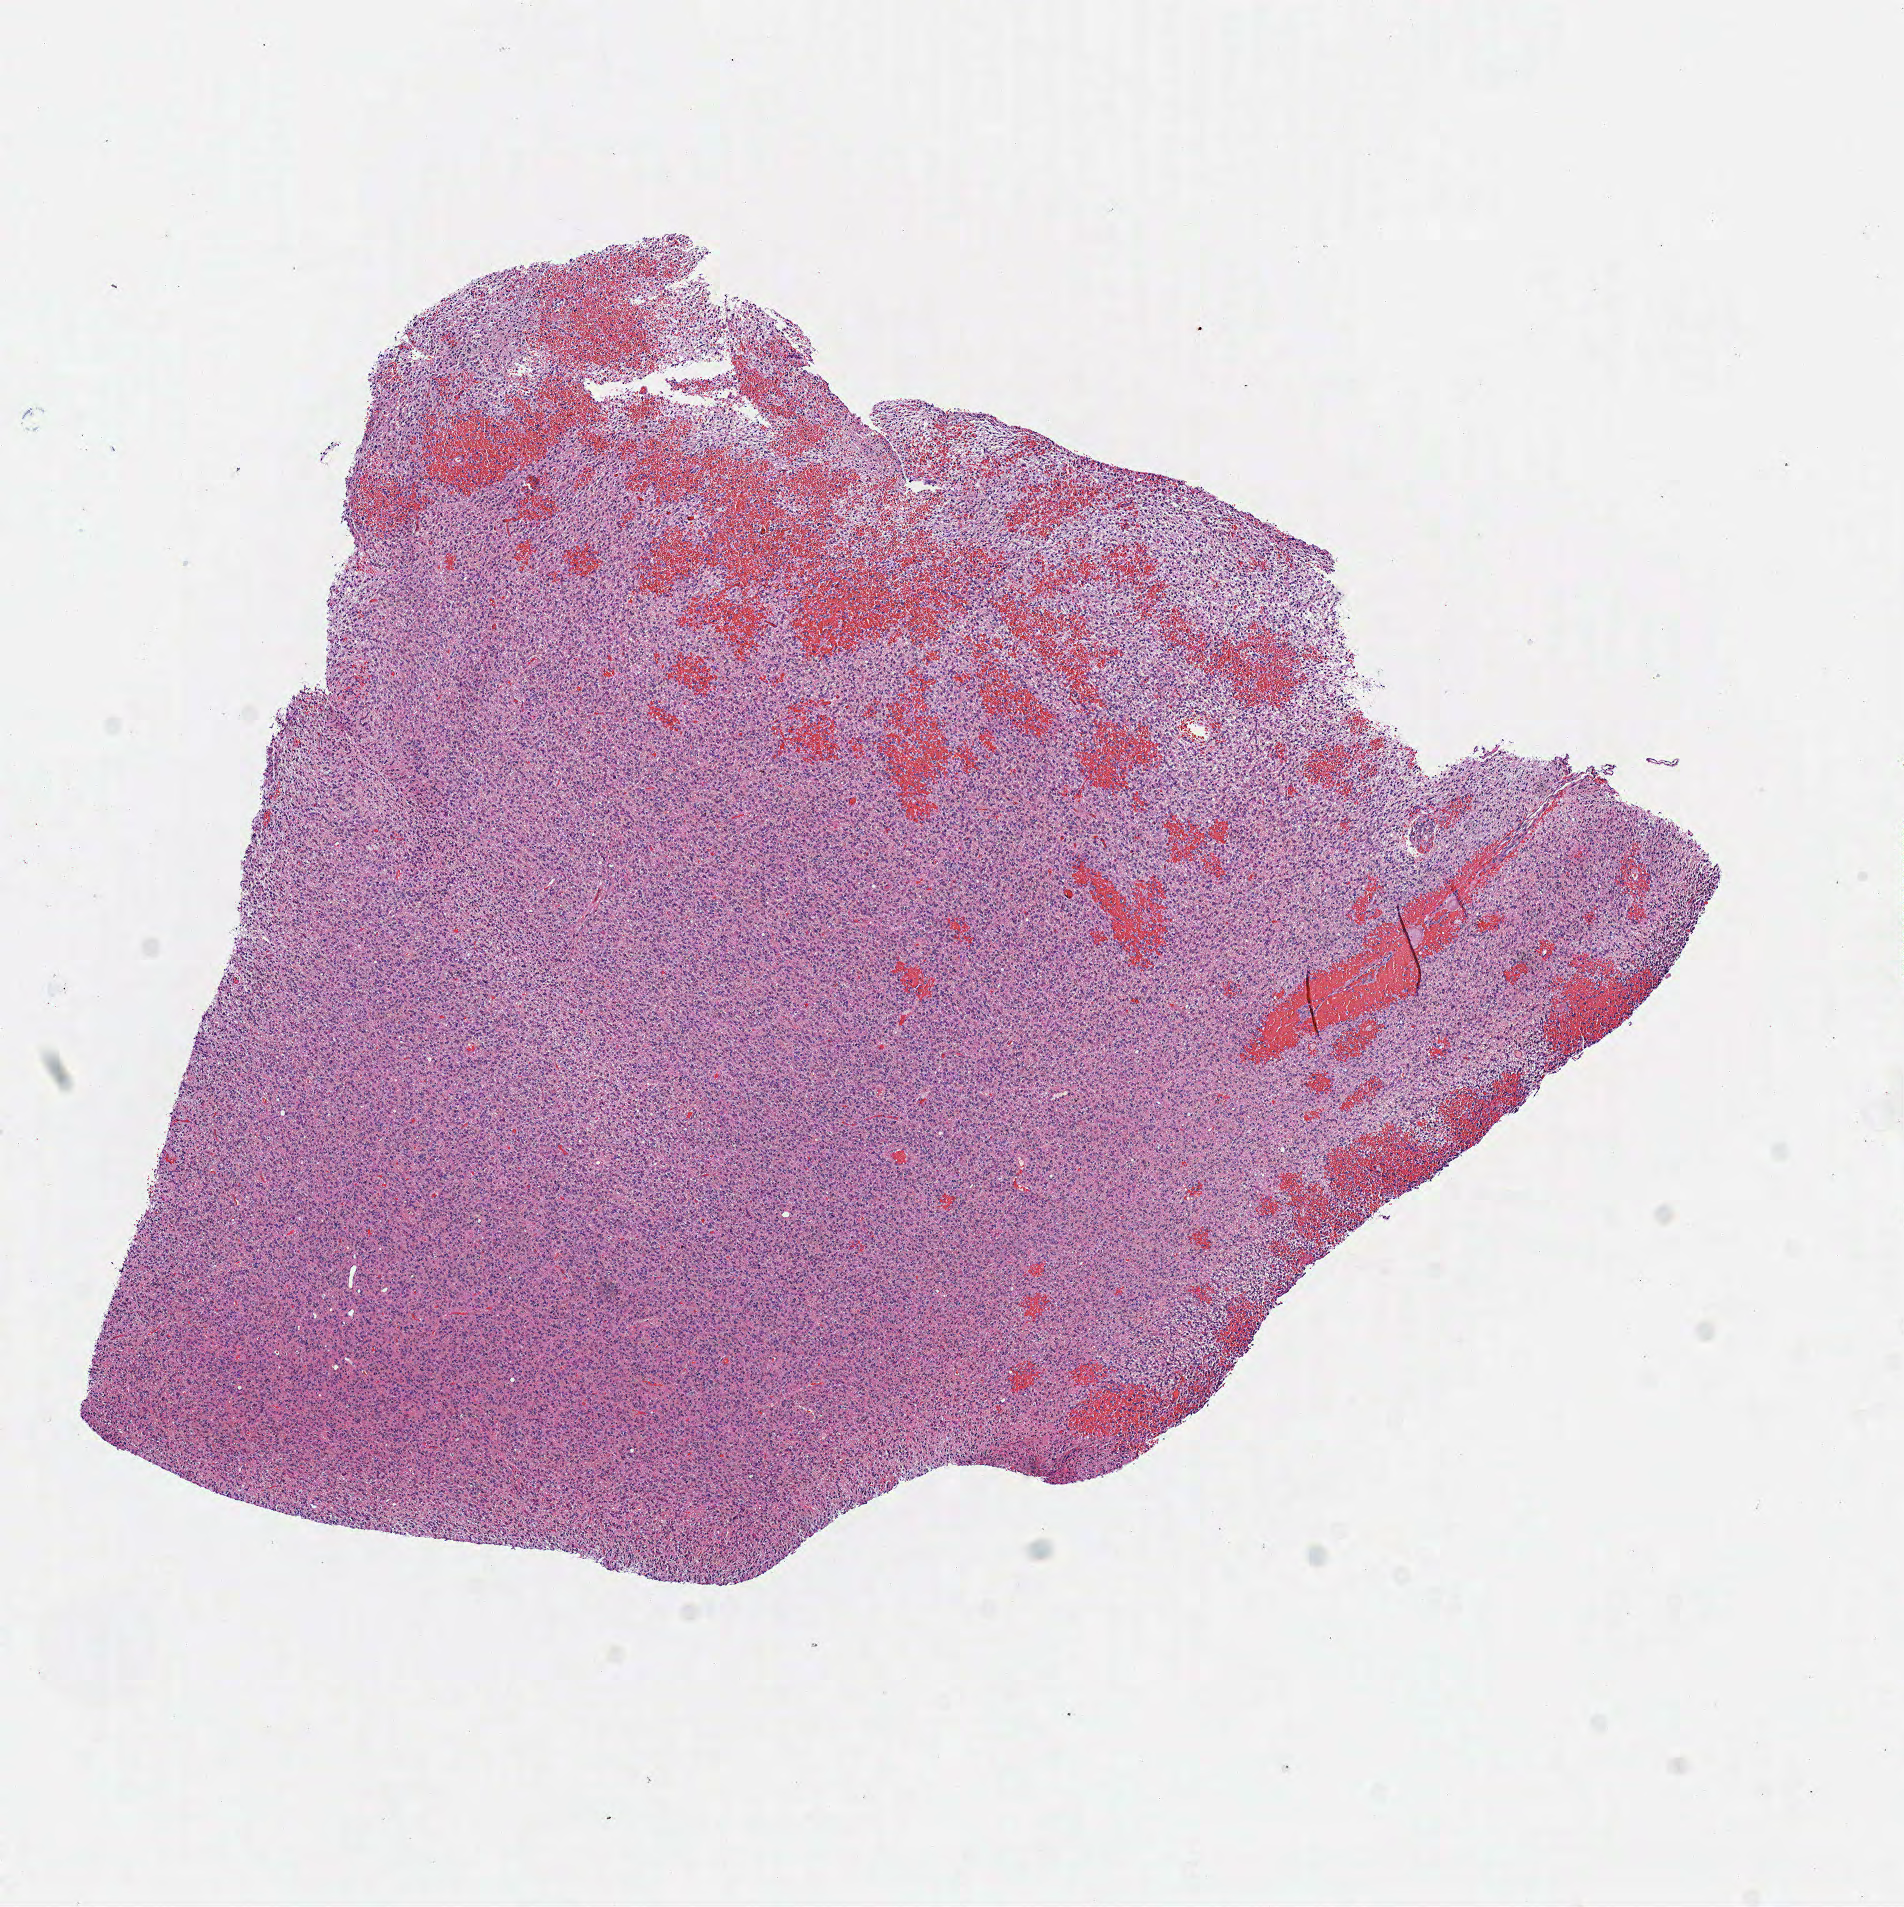
Whole-slide histology image, Hematoxylin and eosin (H&E) stained — low-resolution overview of the scanned area, about 7.5 x 7.5 mm; frozen section from the top of the tissue portion; sample: primary tumour, brain. Male, age 63 years at initial diagnosis. Pathologist review of this section (percent, as recorded): tumour cells 100%, tumour nuclei 80%, normal cells 0%, stromal cells 0%, necrosis 0%.
Histologic diagnosis: Glioblastoma.